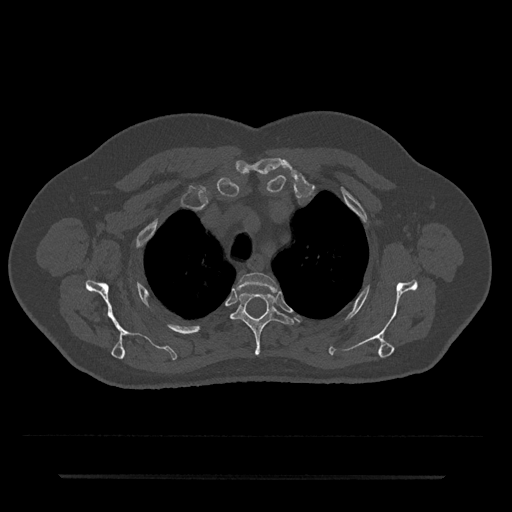
CT including the spine, one axial slice. Position 572 of 797 along the scan axis. Reconstruction kernel Br40s/3. Bone window (W 1800 / L 400 HU). 0.5 mm slice thickness. 512 × 512 image matrix. Patient: male, 69 years. From the clinical record (not read from this slice): primary cancer: prostate.
Annotated regions visible in this slice (semi-automatic segmentation, software-assisted and operator-edited):
- T2 vertebra: bounding box <237,272,278,291> (left, top, right, bottom; pixels)
- T3 vertebra: <231,293,293,356>